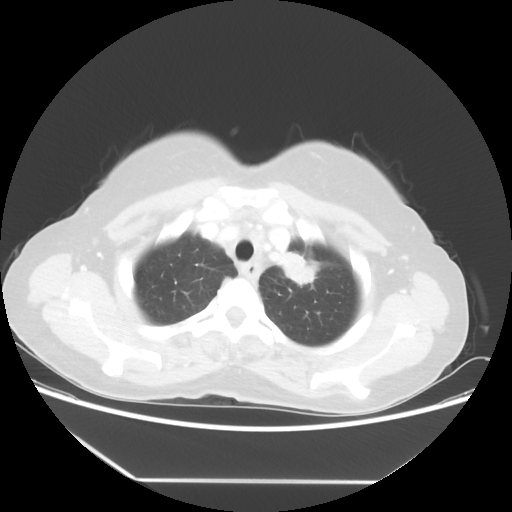
Chest CT, one axial slice; slice 45 of 52 in the series (ordered by position); reconstruction kernel STANDARD; 100 kVp; lung window (W 1500 / L -600 HU); 5 mm slice thickness; 512 × 512 image matrix. Patient: female, 50 years. Case-level facts recorded for this patient, not image findings: clinical TNM (as recorded): T2 N3 M0.
Structures marked on this image (rectangle marked by the reading radiologist):
- lung tumour (recorded histology: adenocarcinoma): box from (x=269, y=239) to (x=326, y=300) px